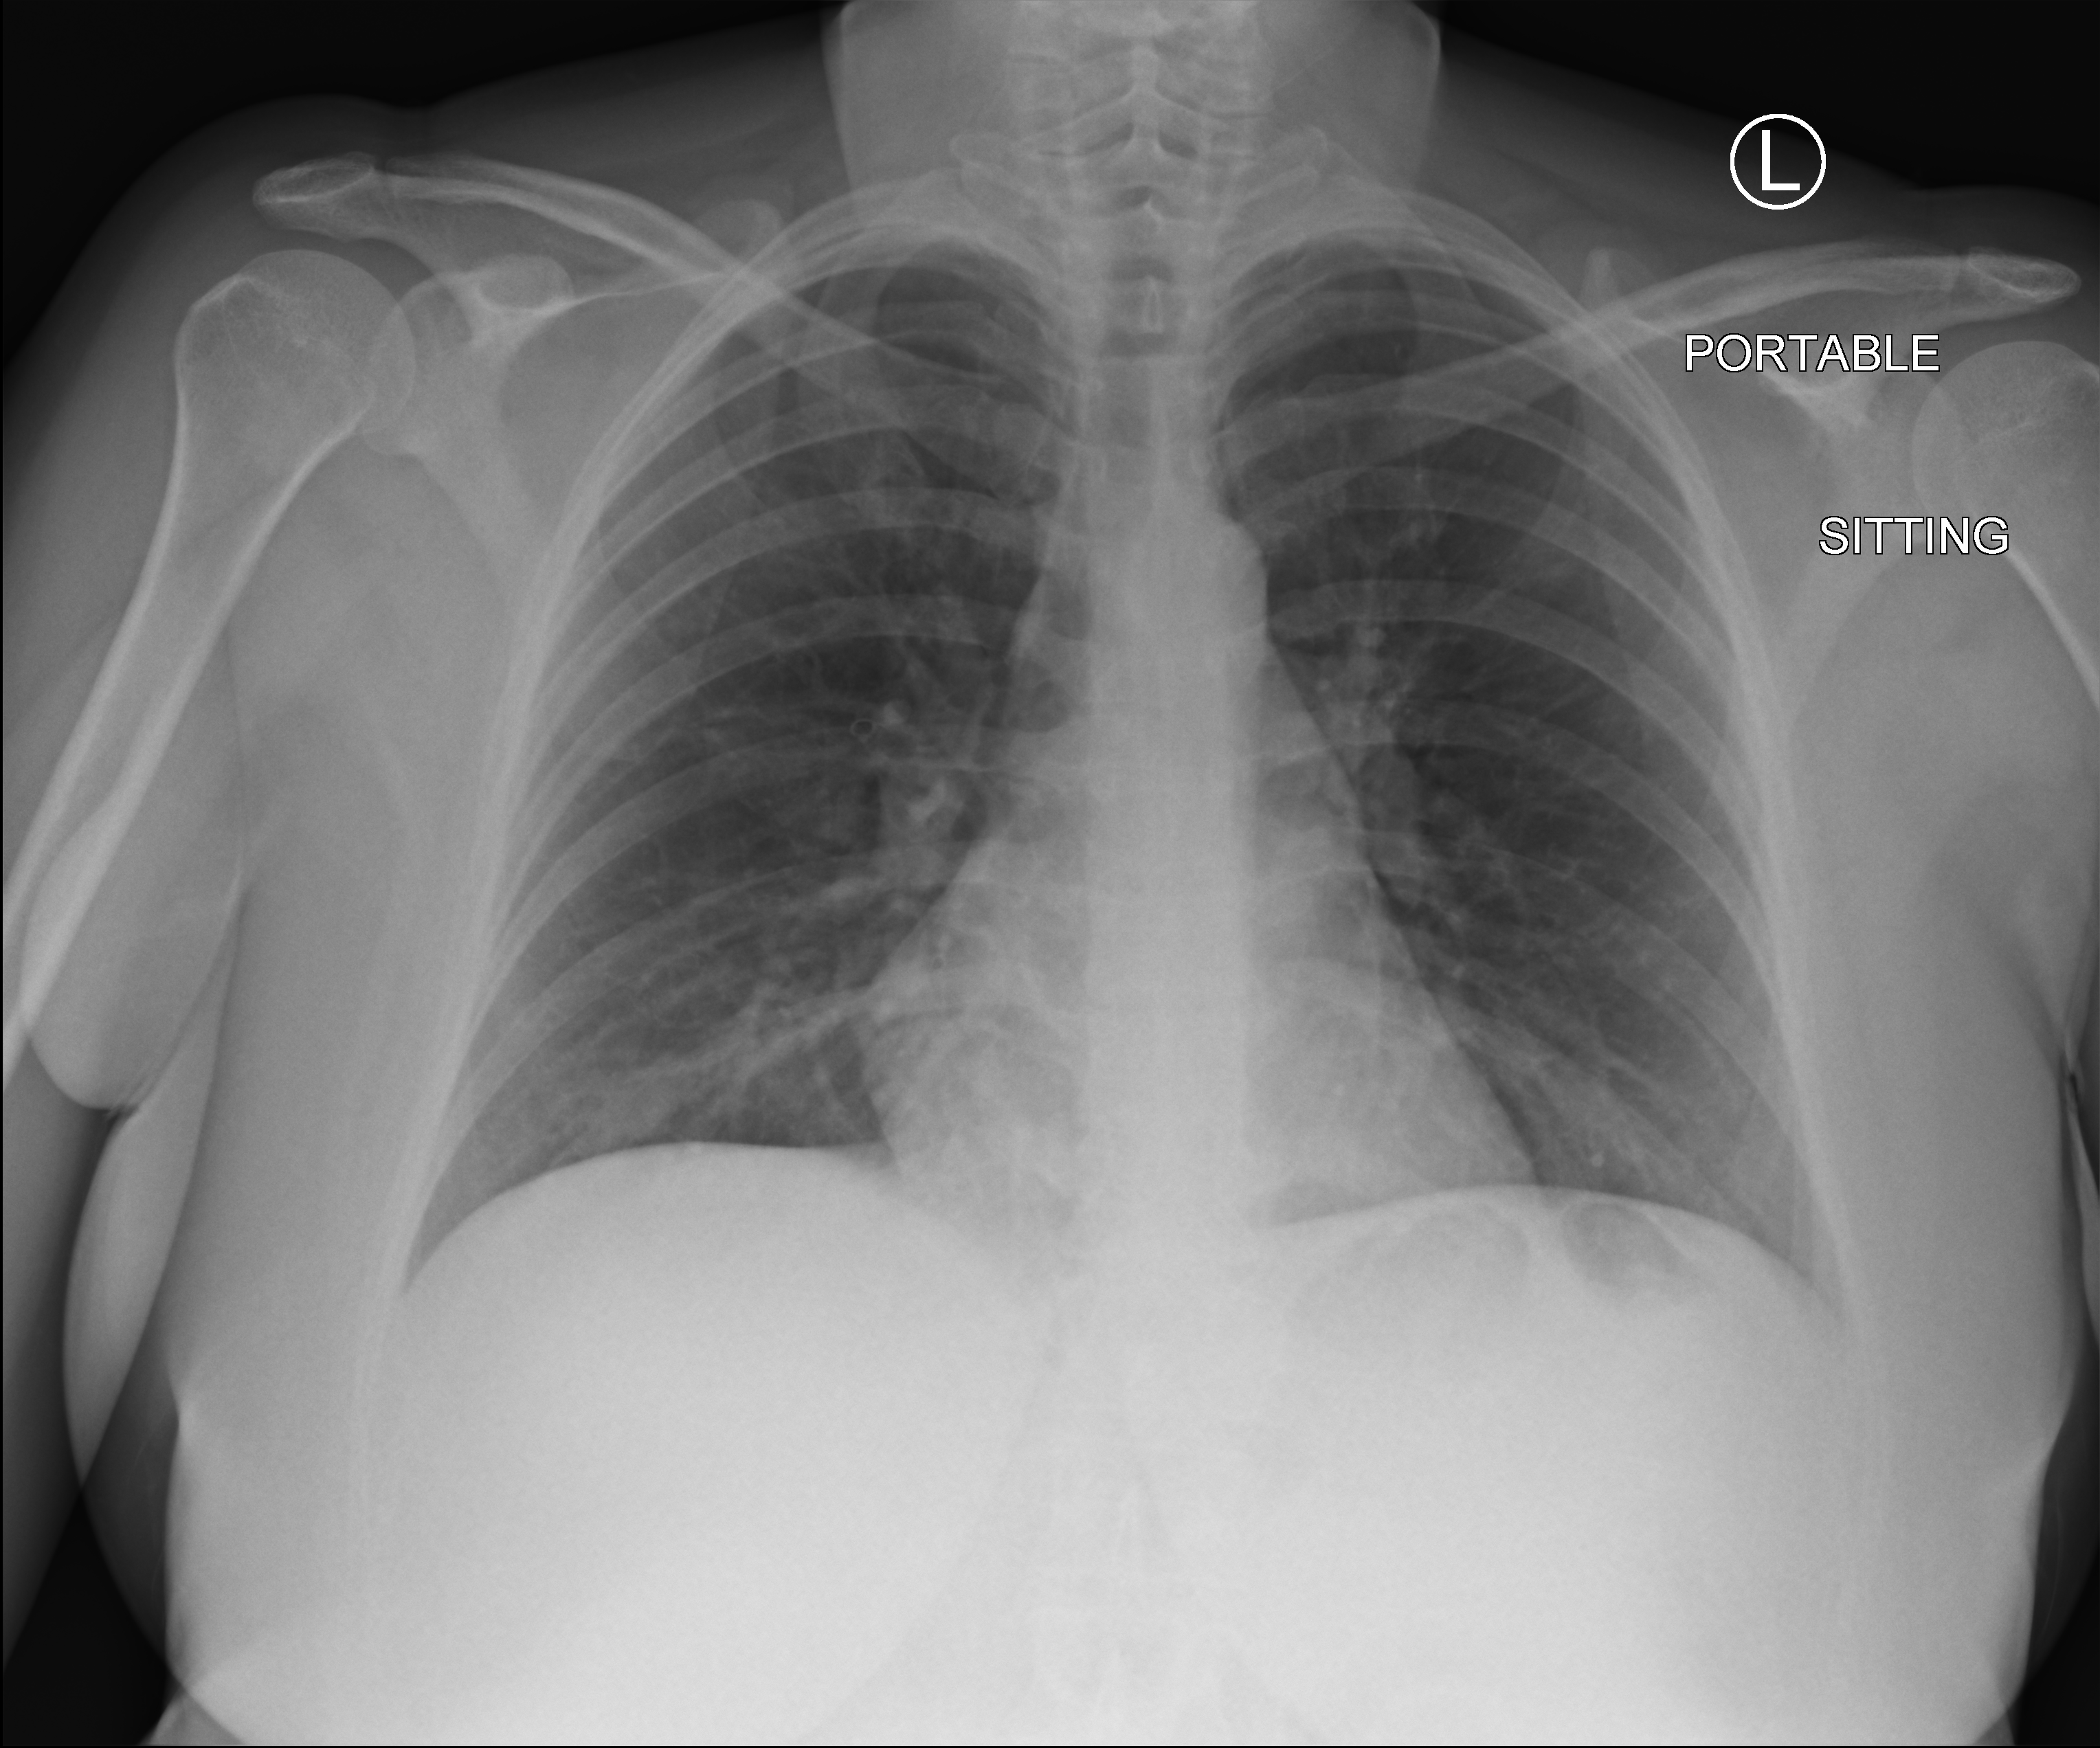
Chest X-ray (portable). Patient hospitalised with COVID-19; female, aged 18–59 years.
Hospital-stay facts (about this admission, not read from this image; timing relative to this image not recorded): admitted to intensive care during this hospital stay: no; mechanically ventilated during this hospital stay: no; length of hospital stay: 1 day.